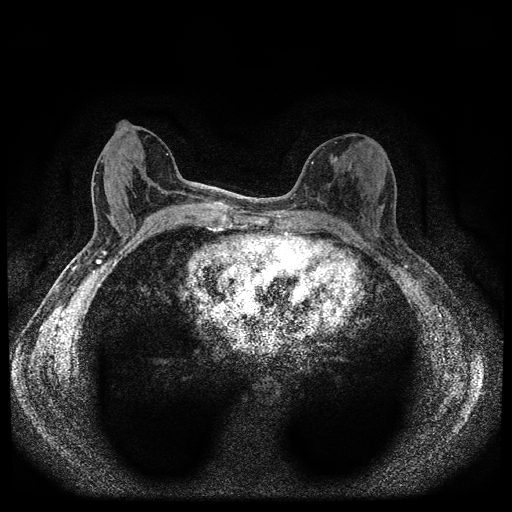
Breast MRI (dynamic contrast-enhanced, multi-phase), one axial slice. Position 43 of 112 along the scan axis. Dynamic contrast-enhanced series, time point 2 of 5 at this slice position (early post-contrast). 1.5 T. TE 2.7 ms, TR 5.4 ms. 2 mm slice thickness. 512 × 512 image matrix, field of view 320 × 320 mm. Female patient, age 61 years.
Annotated regions visible in this slice (semi-automatically segmented with operator editing):
- breast lesion (labelled benign in the annotation): bounding box <330,153,338,166> (left, top, right, bottom; pixels)